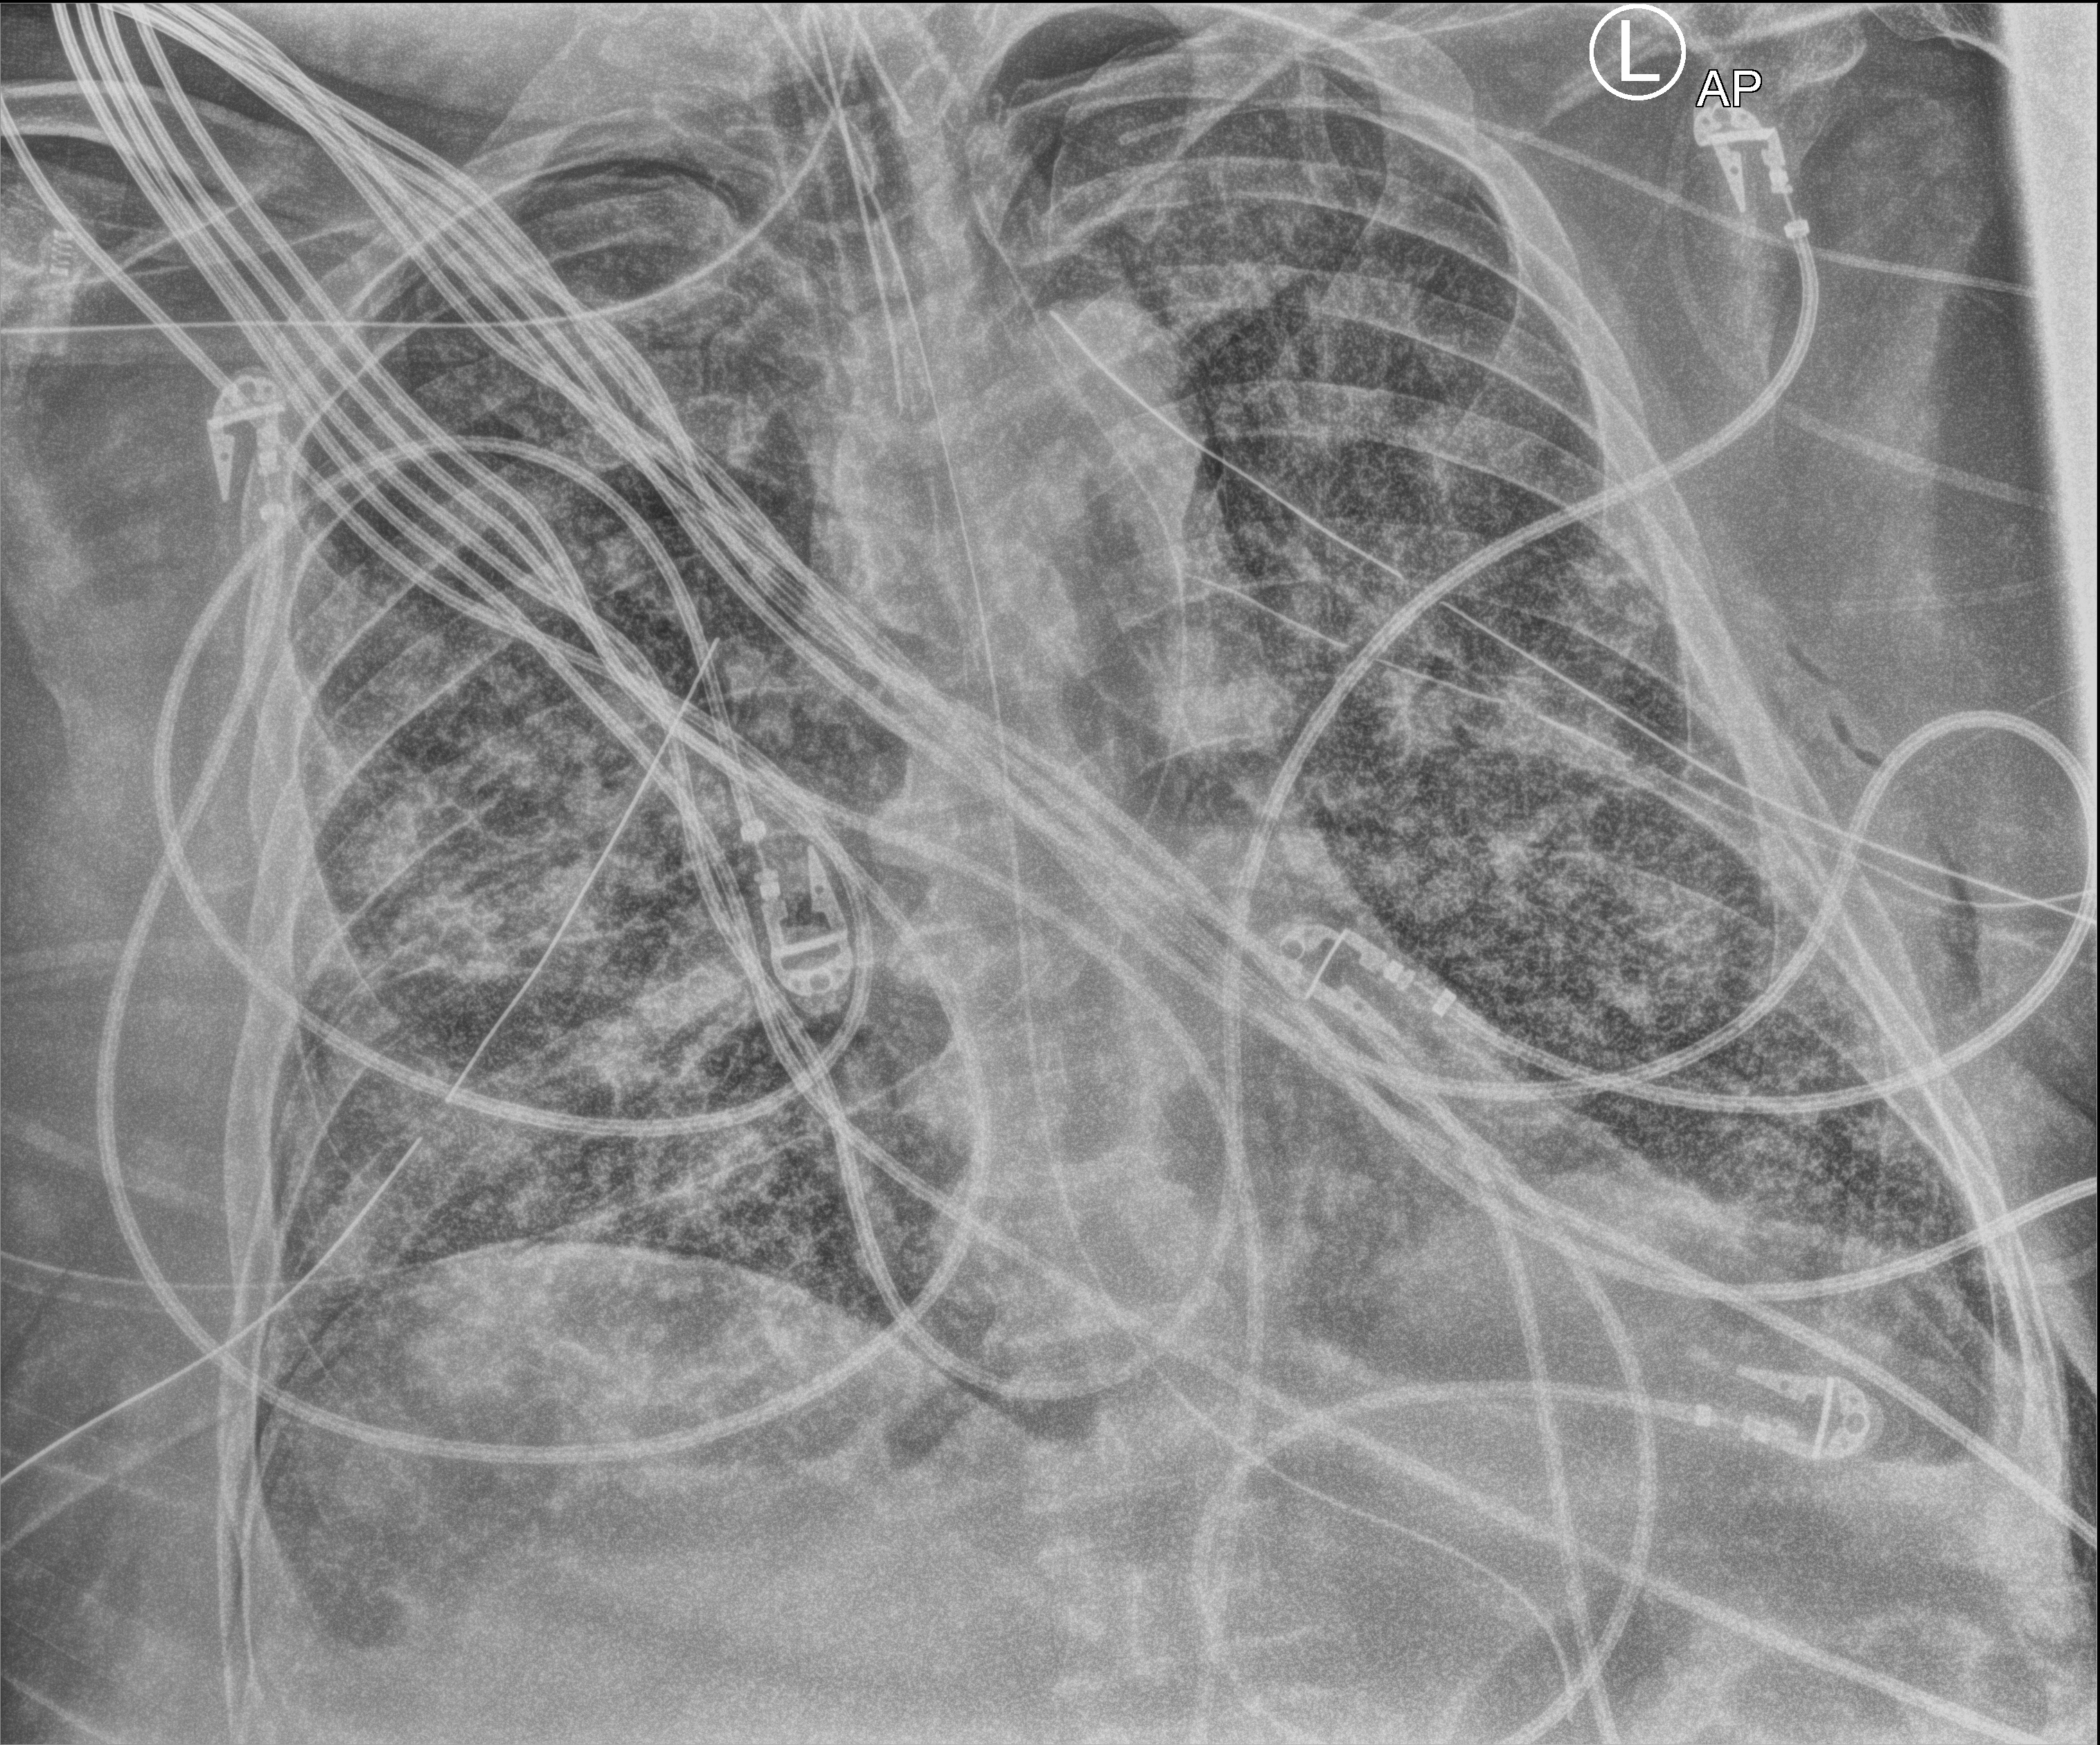
Portable chest radiograph, anteroposterior (AP) projection. Adult patient hospitalised with COVID-19, age 18–59 years.
From the hospital-stay record, not from the radiograph (when in the stay this image was taken is not recorded):
- admitted to intensive care during this hospital stay: yes
- mechanically ventilated during this hospital stay: yes